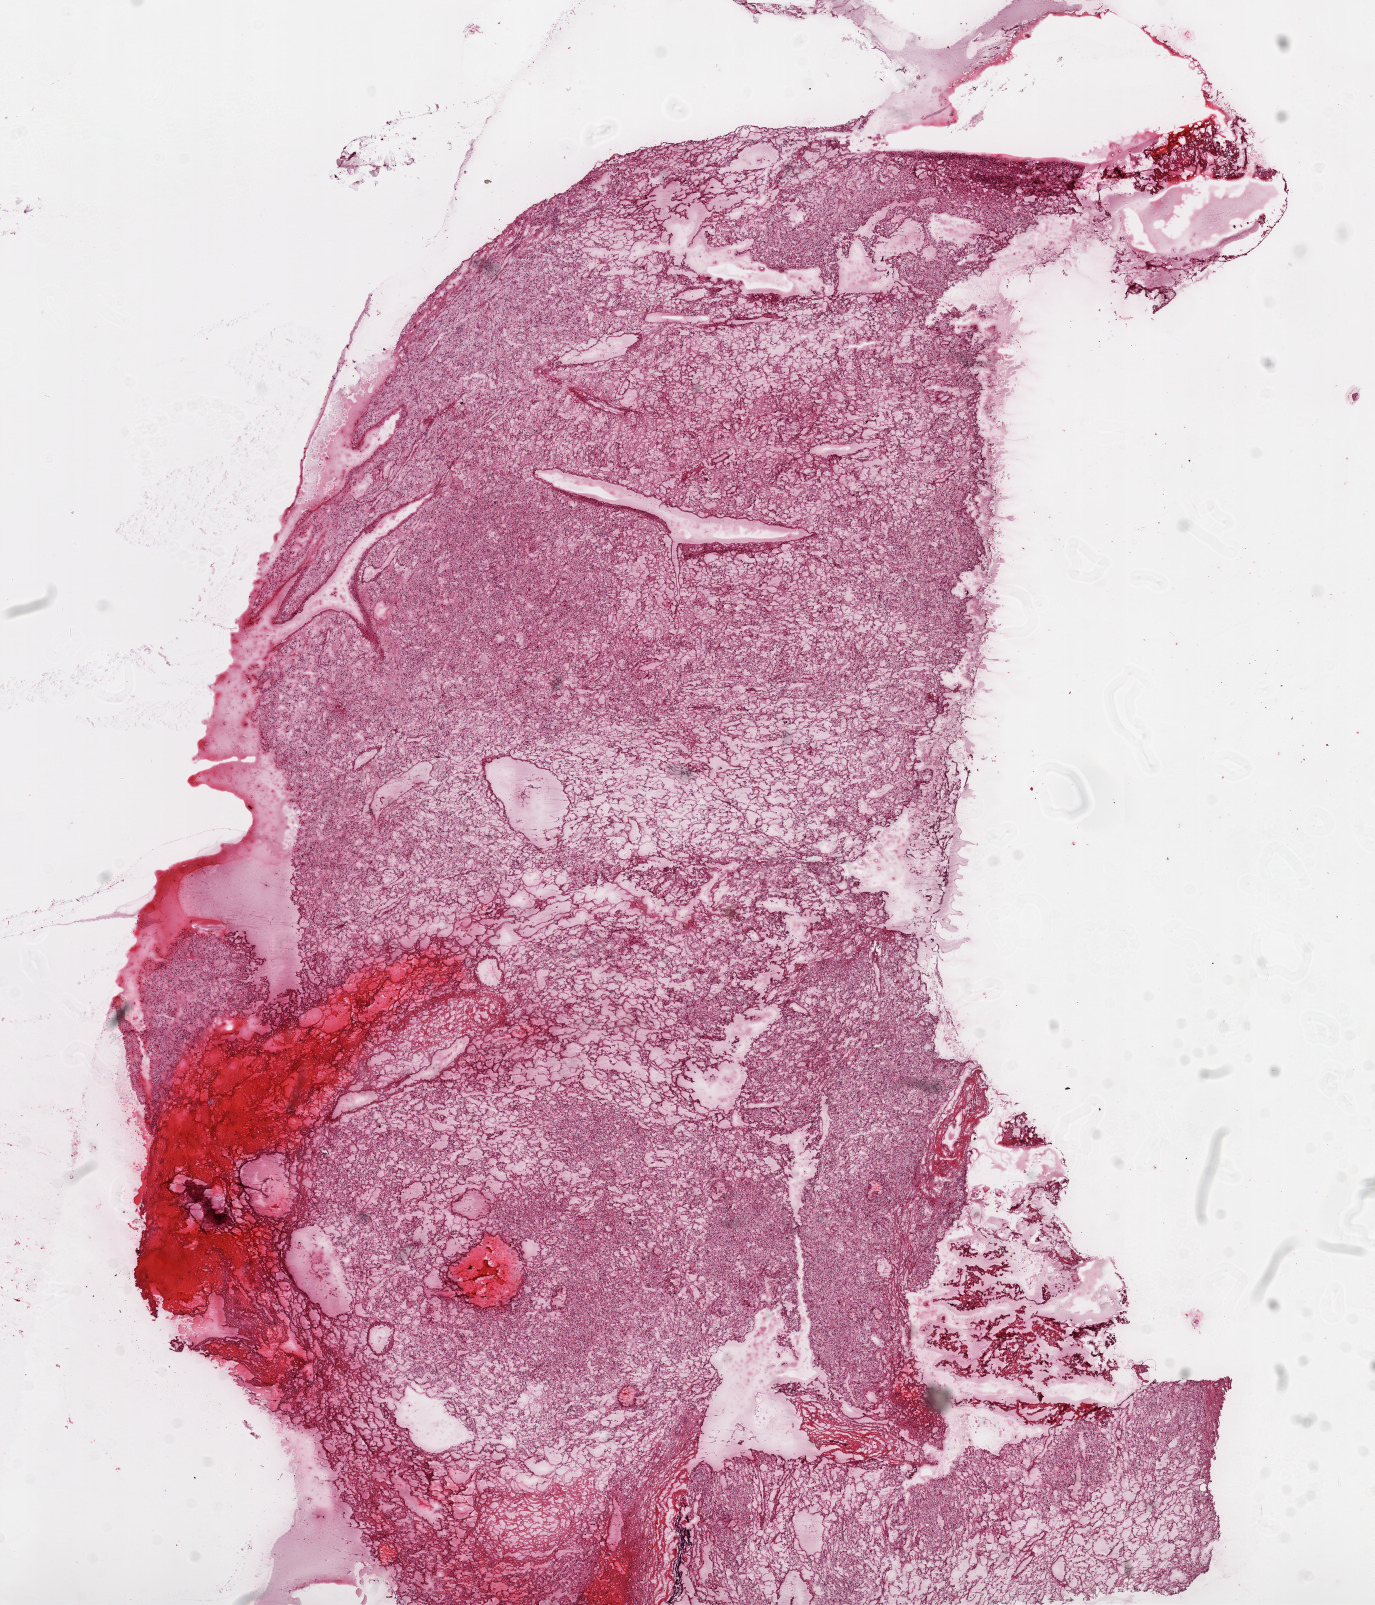
Digitized H&E-stained tissue section (whole slide) — shown as a low-resolution overview of the whole scanned area (about 11.0 x 12.9 mm); frozen section from the top of the tissue portion; primary tumour sample from the kidney. Female patient; age at initial diagnosis 75 years. Histologic grade: G2 (moderately differentiated). Slide review estimates, as recorded: tumour cells 95%, tumour nuclei 85%, normal cells 0%, stromal cells 5%, necrosis 0%.
Histologic diagnosis: Clear cell adenocarcinoma, NOS. AJCC pathologic stage: I. Laterality: right.